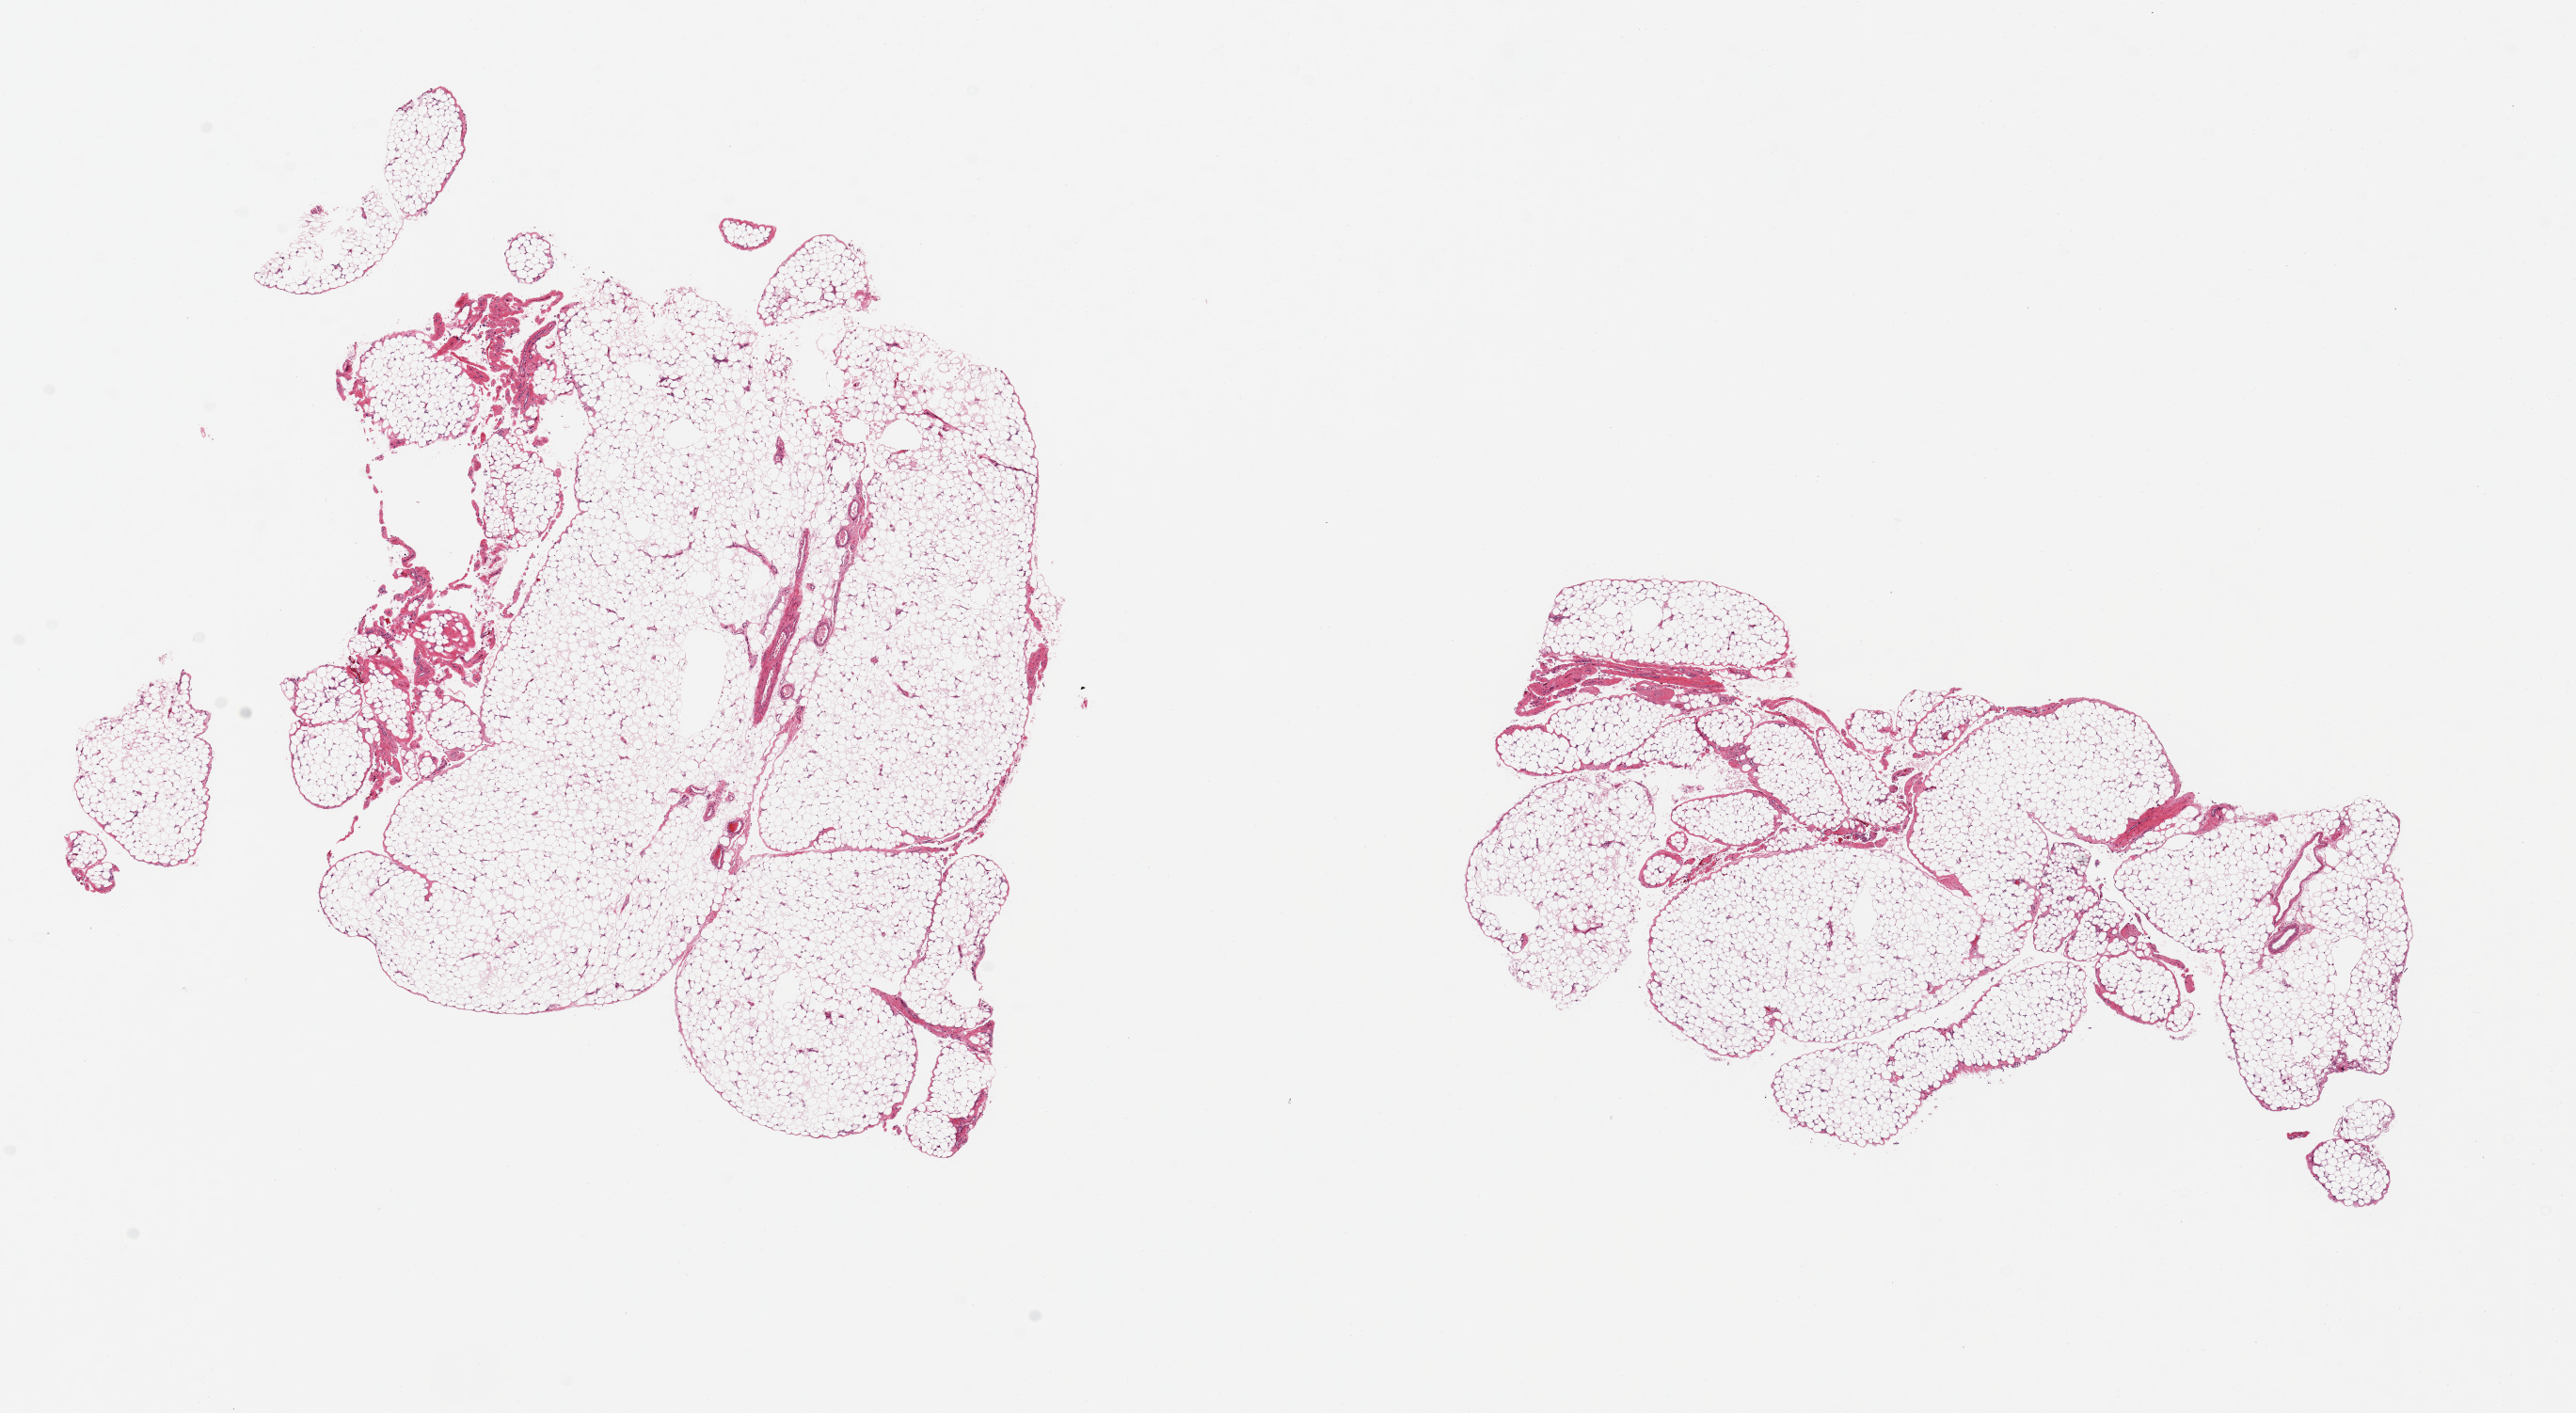
Digitized H&E-stained section, brightfield — a low-resolution overview of the entire scanned area, about 21.7 x 11.9 mm (acquisition: 20x scan), PAXgene-fixed, paraffin-embedded tissue, sampled site (target tissue): omentum, tissue donor sample.
* review note (as recorded): 2 pieces, 8.5x8 & 7x4mm; well fixed, no artifacts